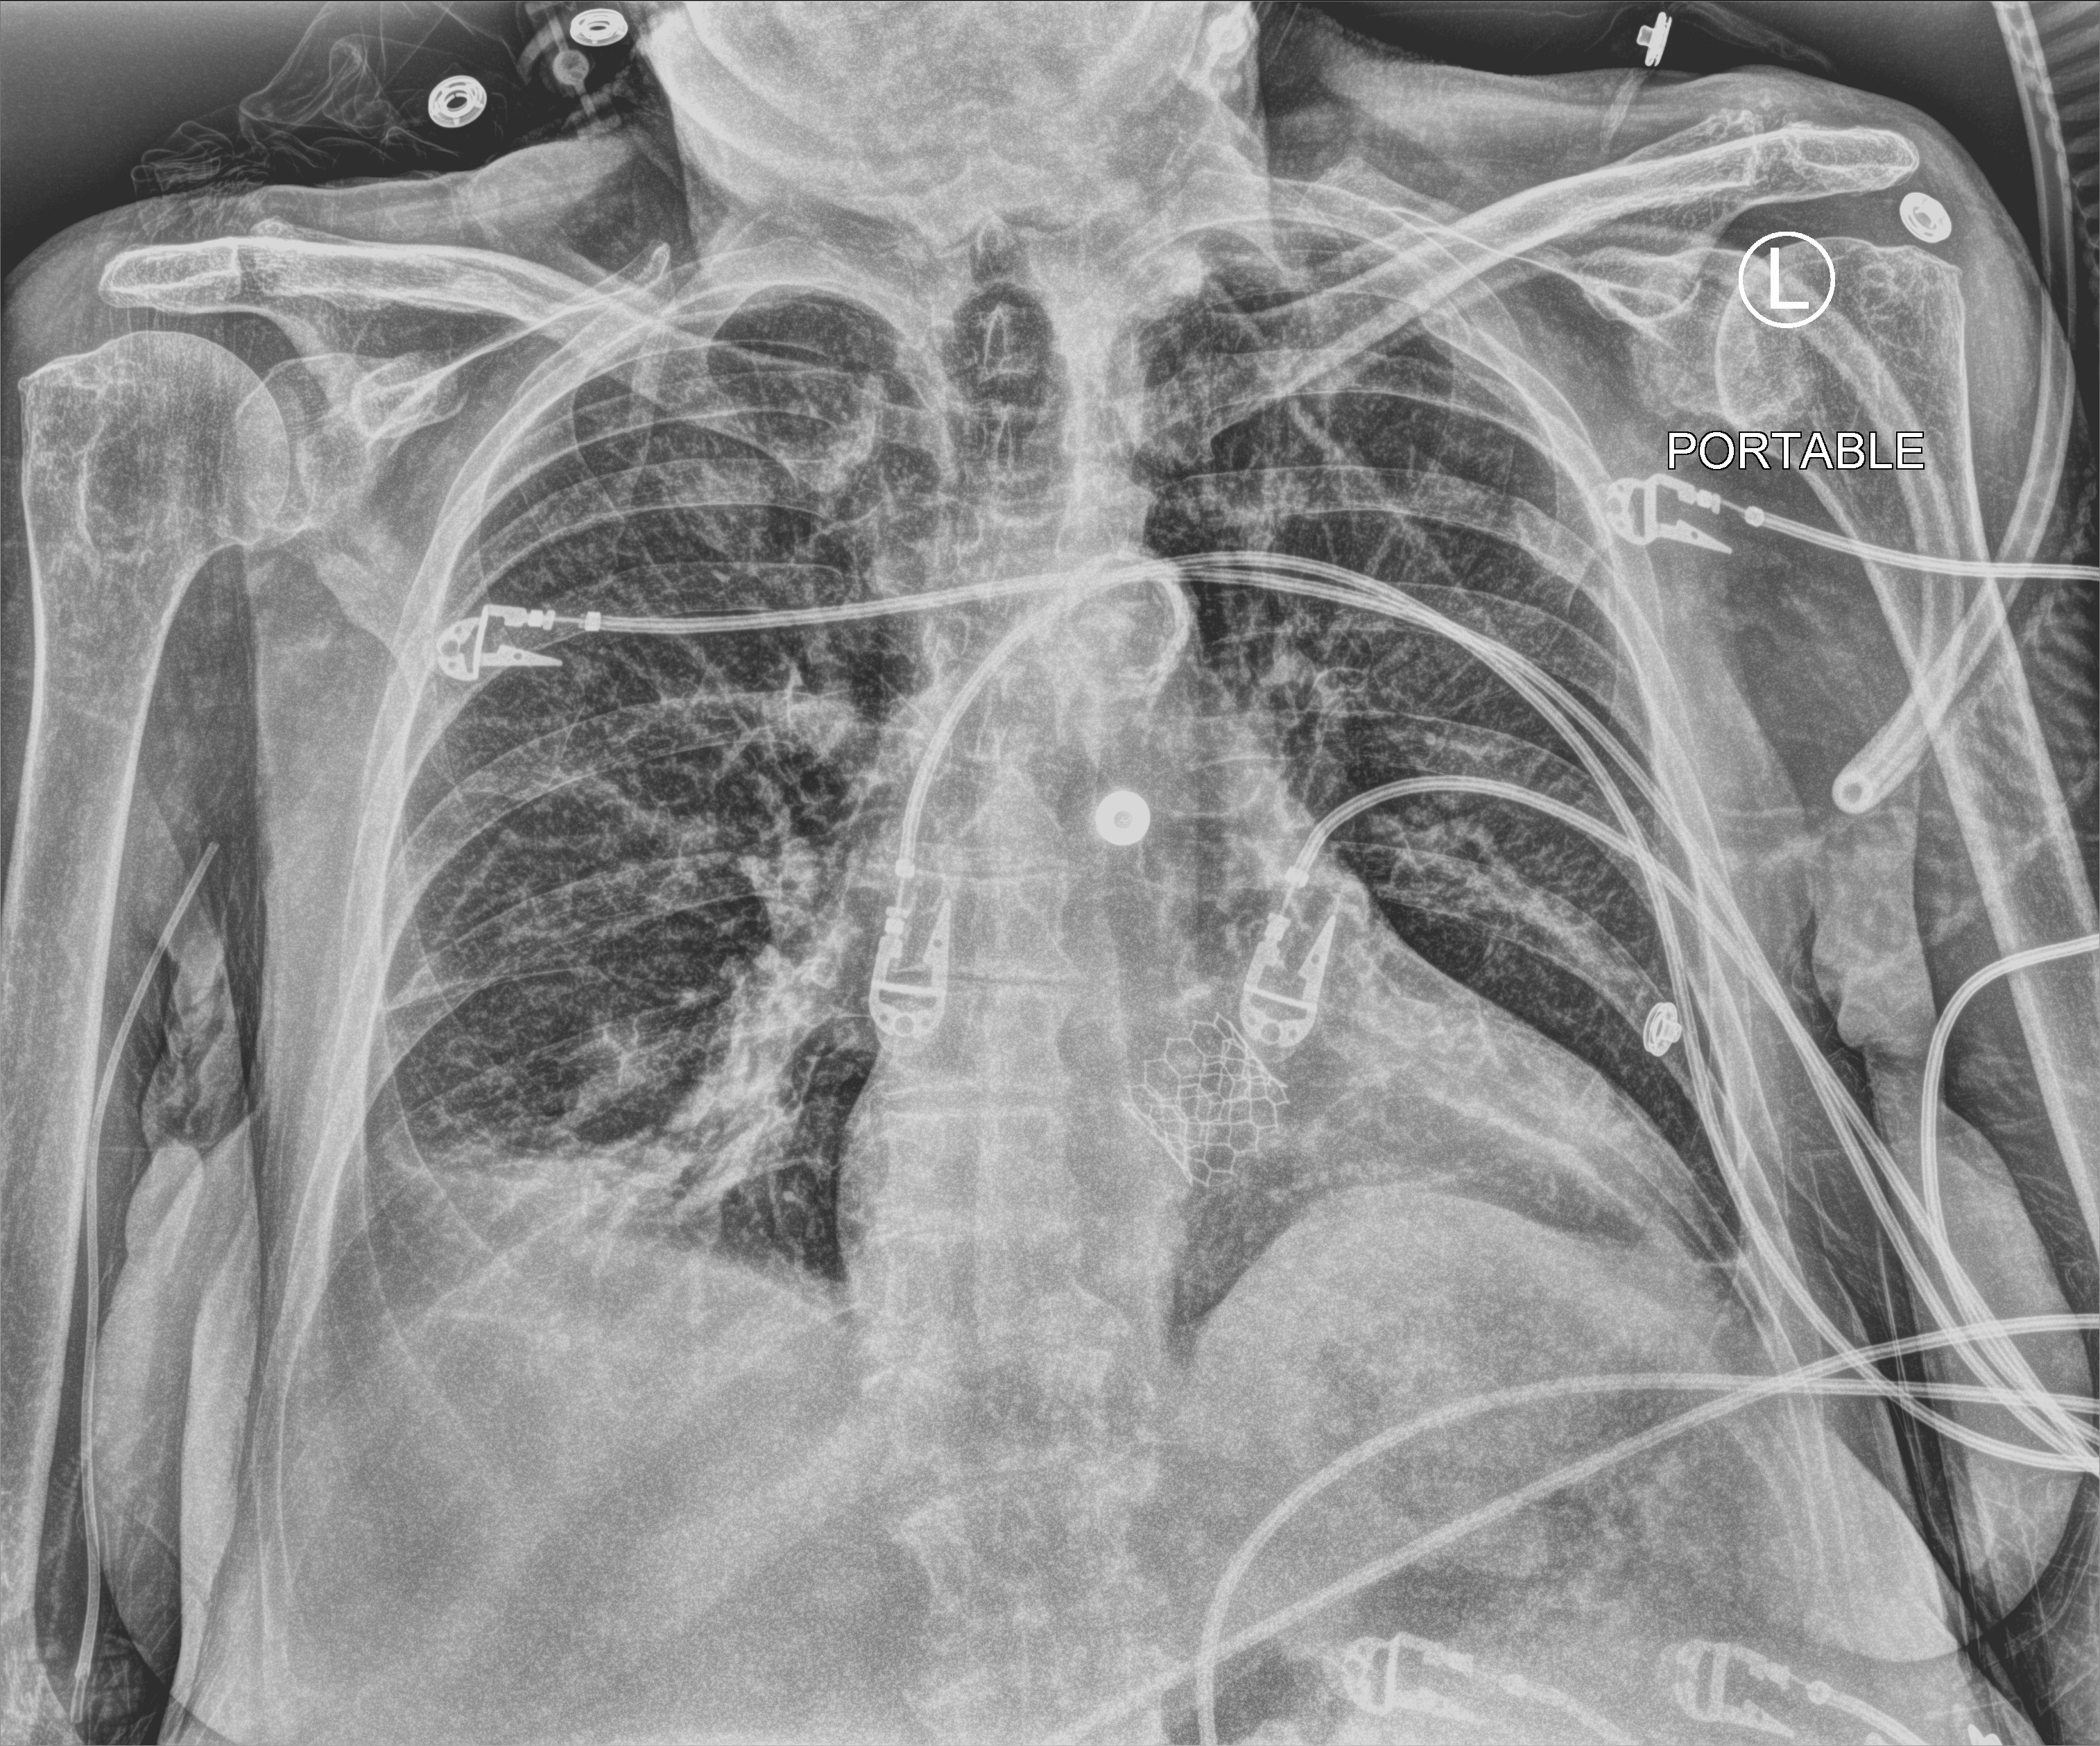
Portable chest radiograph, anteroposterior (AP) projection. Female patient hospitalised with COVID-19, age 75–90 years.
From the hospital-stay record, not from the radiograph (when in the stay this image was taken is not recorded):
- admitted to intensive care during this hospital stay: no
- chronic kidney disease (admission record): no